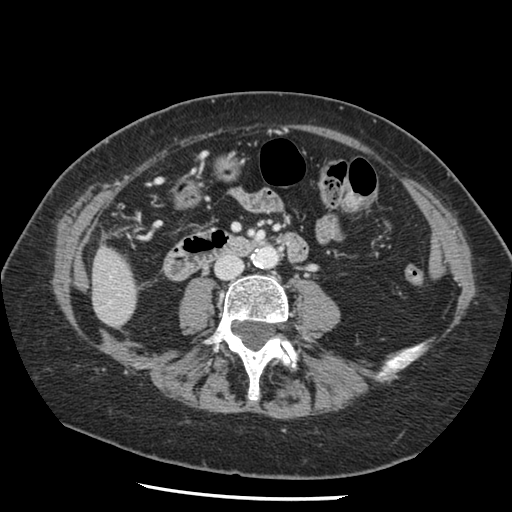
Contrast-enhanced abdominal CT, one axial slice. Slice 23 of 148 in the series (ordered by position). 120 kVp. Intravenous contrast given. Soft-tissue window (W 400 / L 40 HU). 512 × 512 image matrix. Female patient, age 85 years. From the clinical record (not read from this slice): diagnosis: colorectal cancer liver metastases, imaged before liver resection; multiple liver metastases: no; largest metastasis: 0.9 cm.
Outlined on this slice (expert manual segmentation):
- liver: bounding box [x1, y1, x2, y2] px = [93, 249, 137, 327]
- planned liver remnant (the part of the liver to remain after resection): [93, 249, 137, 326]